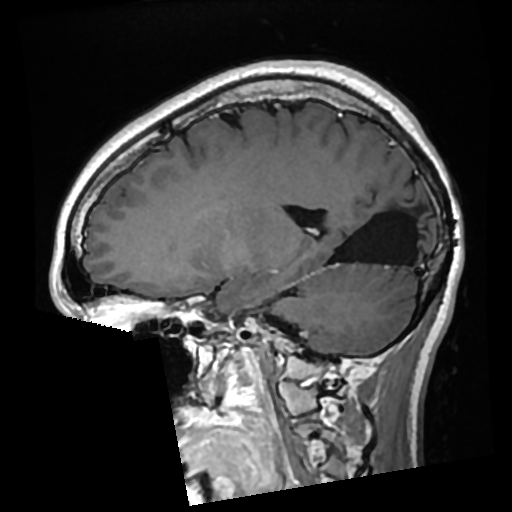
Brain MRI from a brain-tumour surgery series, one sagittal slice. Slice 112 of 276 in the series (ordered by position). T1-weighted post-contrast. 0.7 mm slice thickness. 512 × 512 image matrix, field of view 250 × 250 mm. From the clinical record (not read from this slice): histopathology: Glioma with ependymal features; WHO grade: 2; tumour location: Left Parietal.
Annotated regions visible in this slice (outlined manually by an expert reader):
- previous resection cavity: bounding box (x1, y1, x2, y2) in pixels: (334, 194, 422, 266)